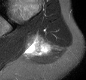
MRI of an extremity soft-tissue mass, one axial slice. Slice 17 of 30 in the series (ordered by position). STIR. MR volume resampled by the dataset authors to the PET/CT grid (not the native acquisition matrix). 86 × 80 image matrix, field of view 84 × 78 mm. Female patient. From the clinical record (not read from this slice): histological type: malignant fibrous histiocytoma; grade: low; site of the primary tumour: left arm.
Annotated regions visible in this slice (expert contour drawn on MRI and transferred to this co-registered scan by the dataset authors):
- gross tumour volume (mass): bounding box <26,31,50,57> (left, top, right, bottom; pixels)